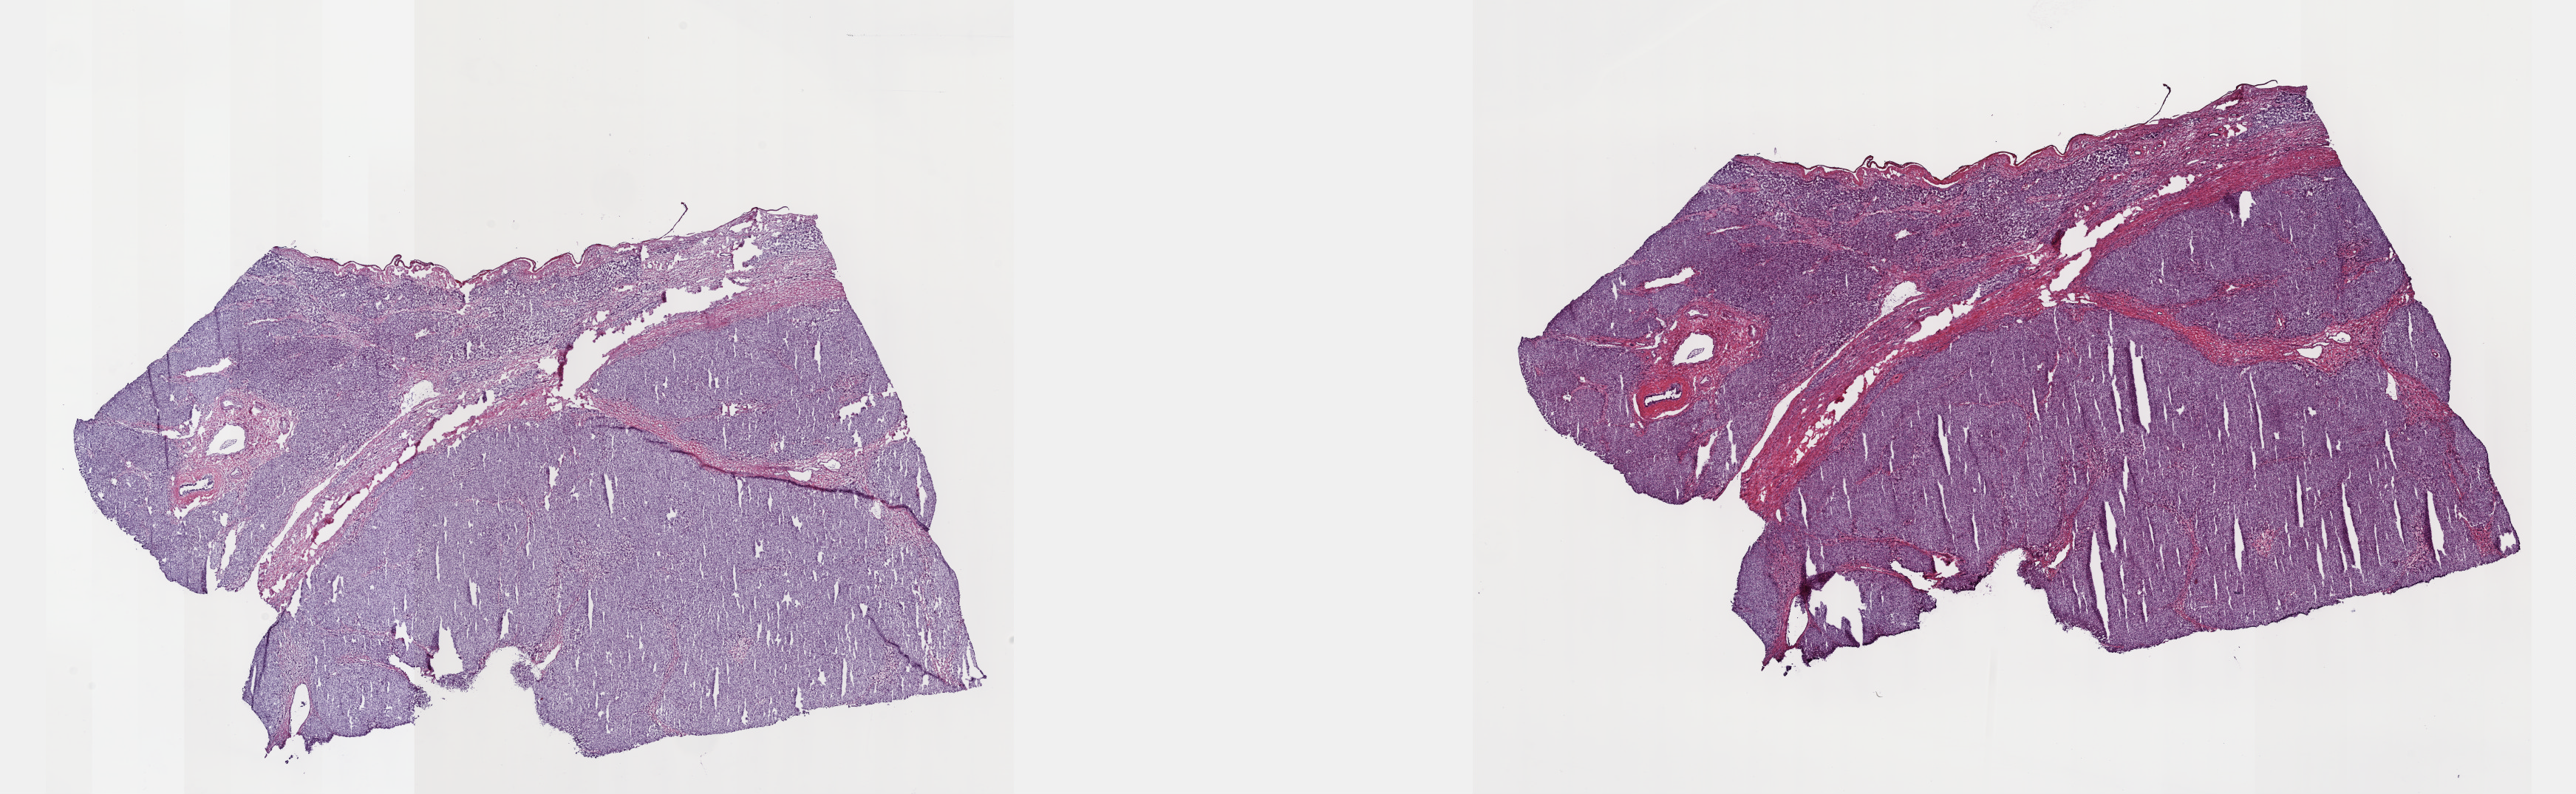
Whole-slide histology image, H&E-stained, whole scanned area (about 28.2 x 8.7 mm) shown as a low-resolution overview, frozen section from the top of the tissue portion, sample: primary tumour, liver. Female patient; age at initial diagnosis 69 years. Composition of this section per pathologist review: tumour cells 100%, tumour nuclei 75%.
Diagnosis: Hepatocellular carcinoma, NOS.